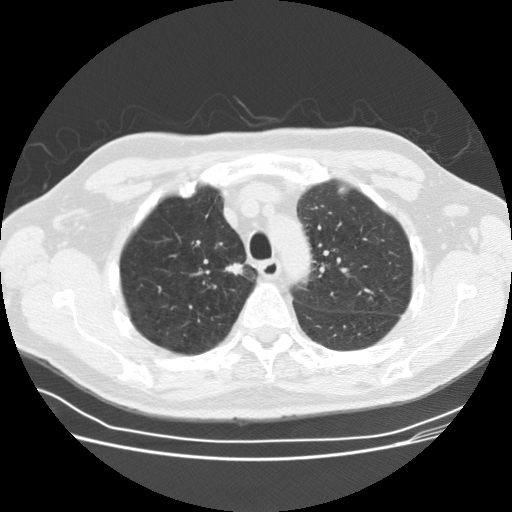
Low-dose screening chest CT, one axial slice. Reconstruction kernel STANDARD. Lung window (W 1500 / L -600 HU). 512 × 512 image matrix, field of view 360 × 360 mm.
Structures marked on this image (expert manual segmentation):
- lesion 1 (tumor, upper lobe of right lung): bounding box <225,263,244,275> (left, top, right, bottom; pixels)